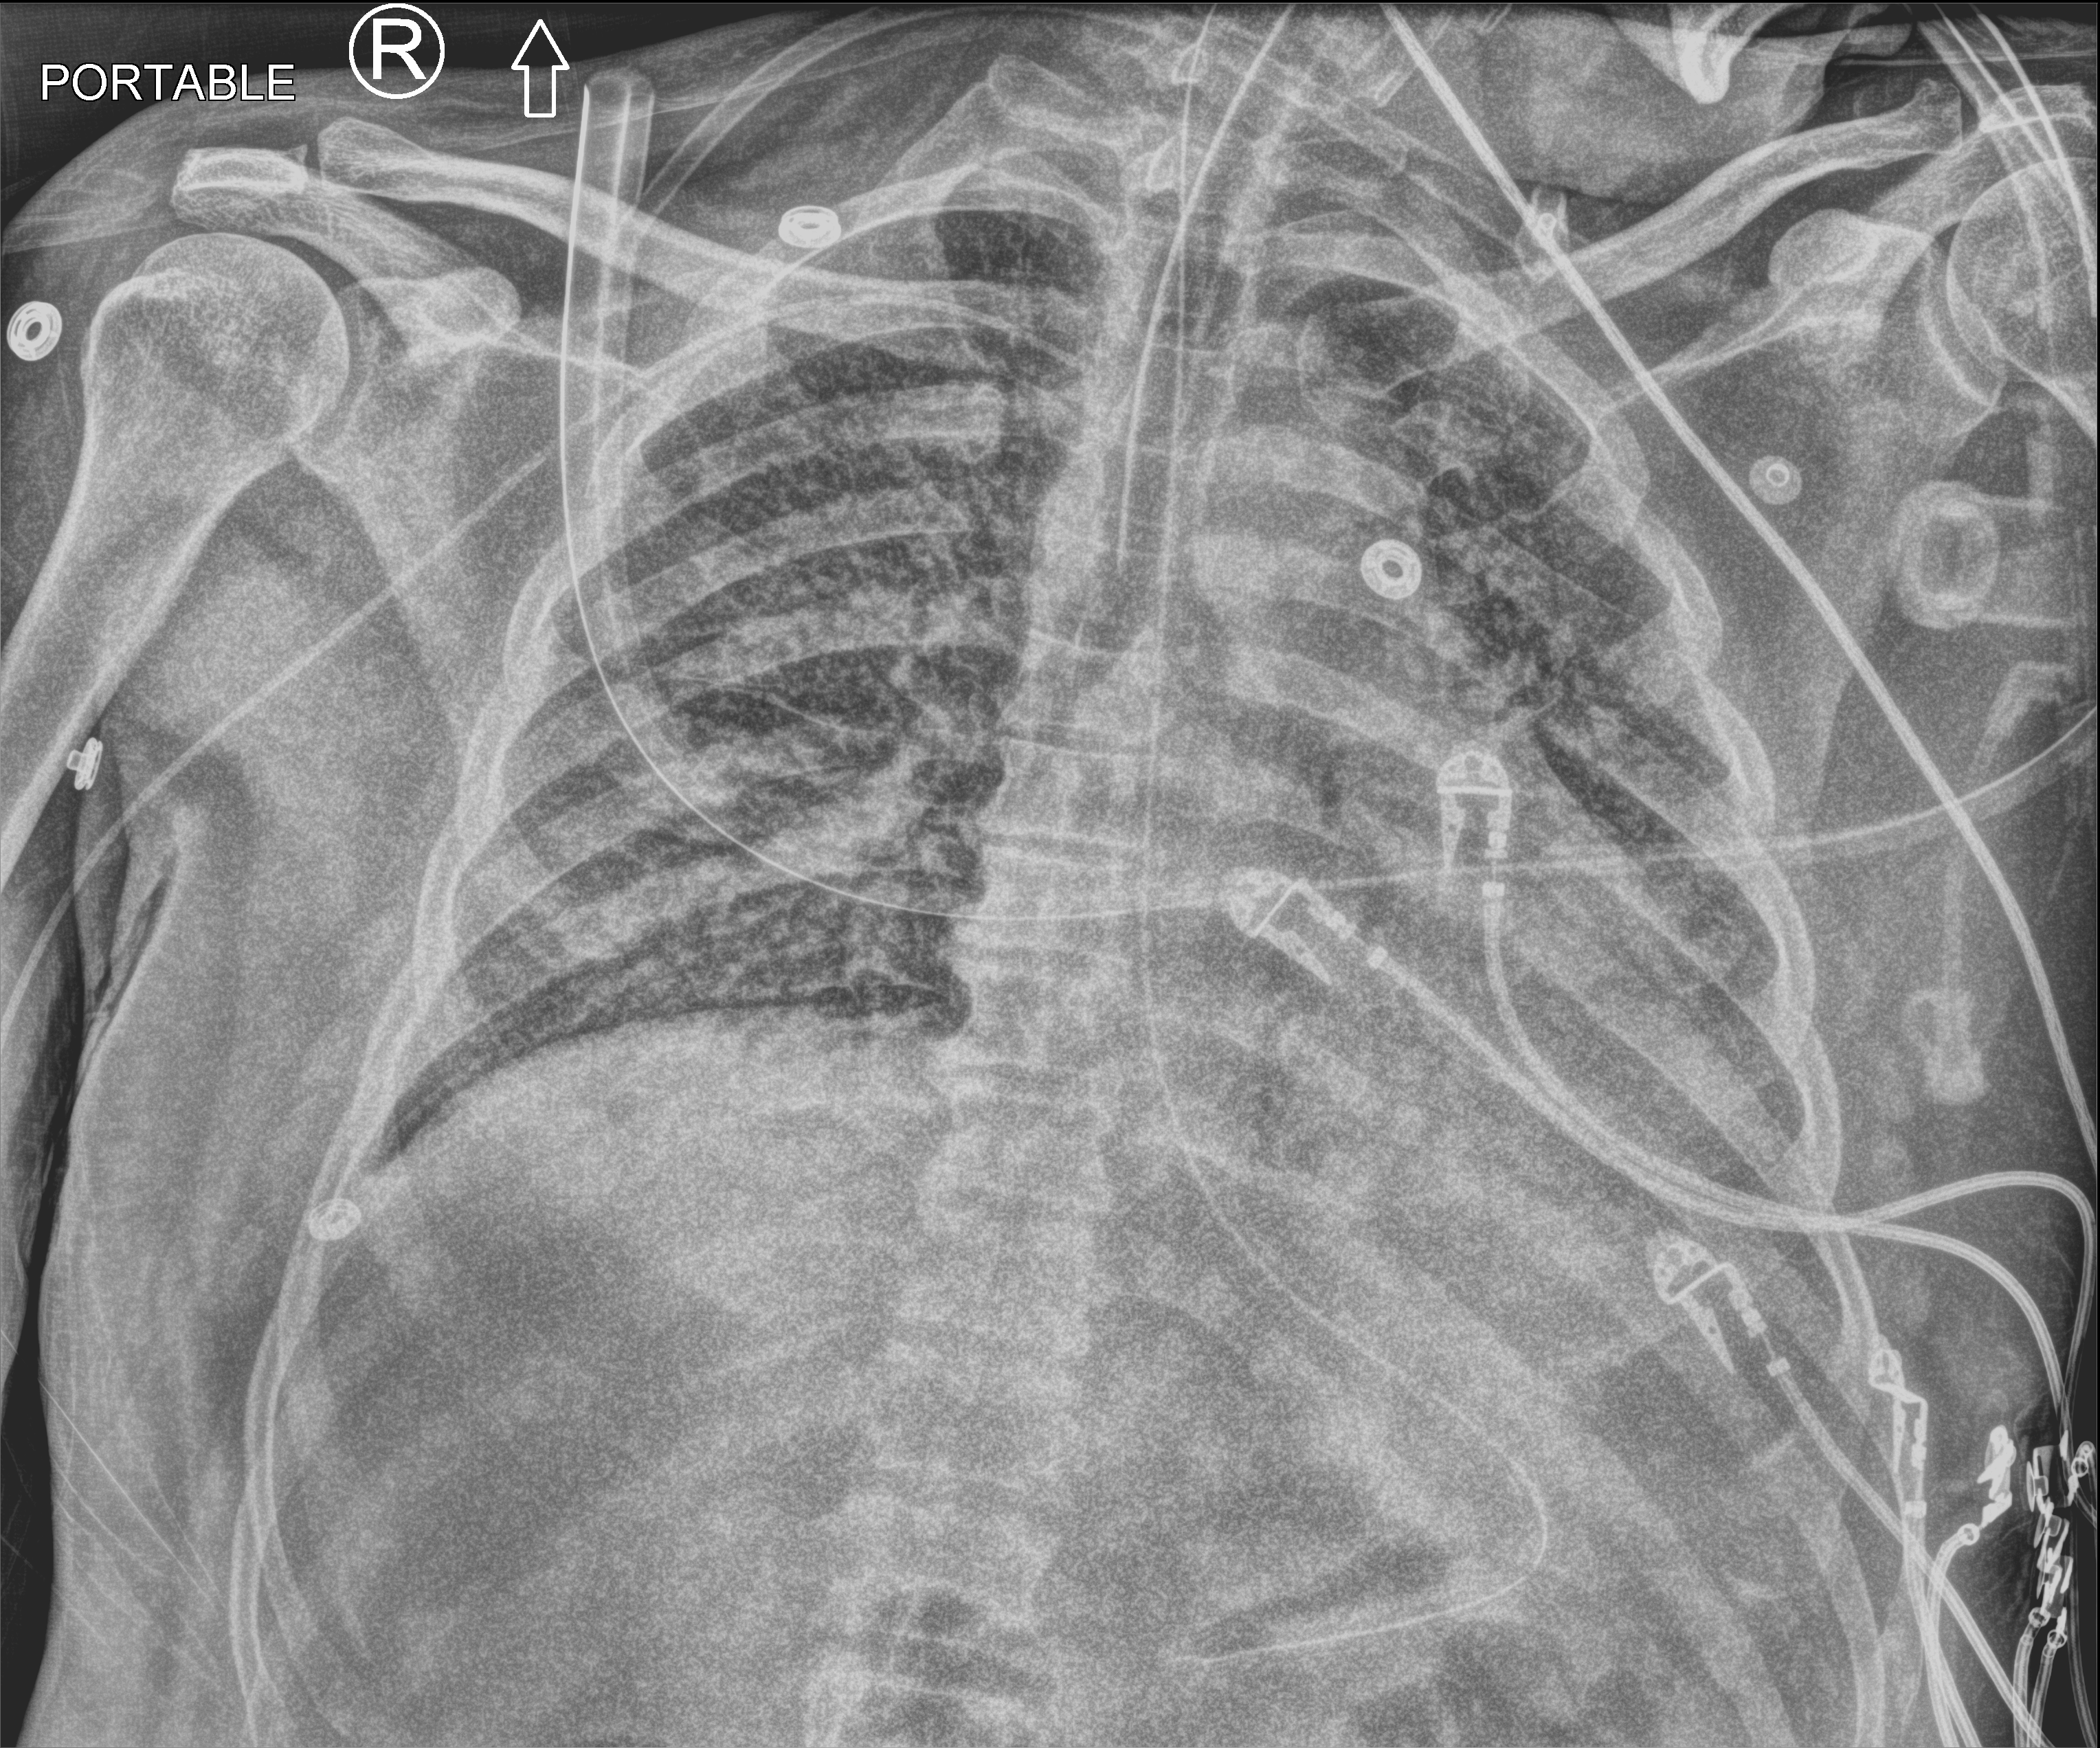
Chest X-ray (portable); anteroposterior (AP) projection. Patient hospitalised with COVID-19; male, aged 18–59 years.
Admission-level facts for this patient (not findings on this image; timing relative to this image not recorded): admitted to intensive care during this hospital stay: yes.